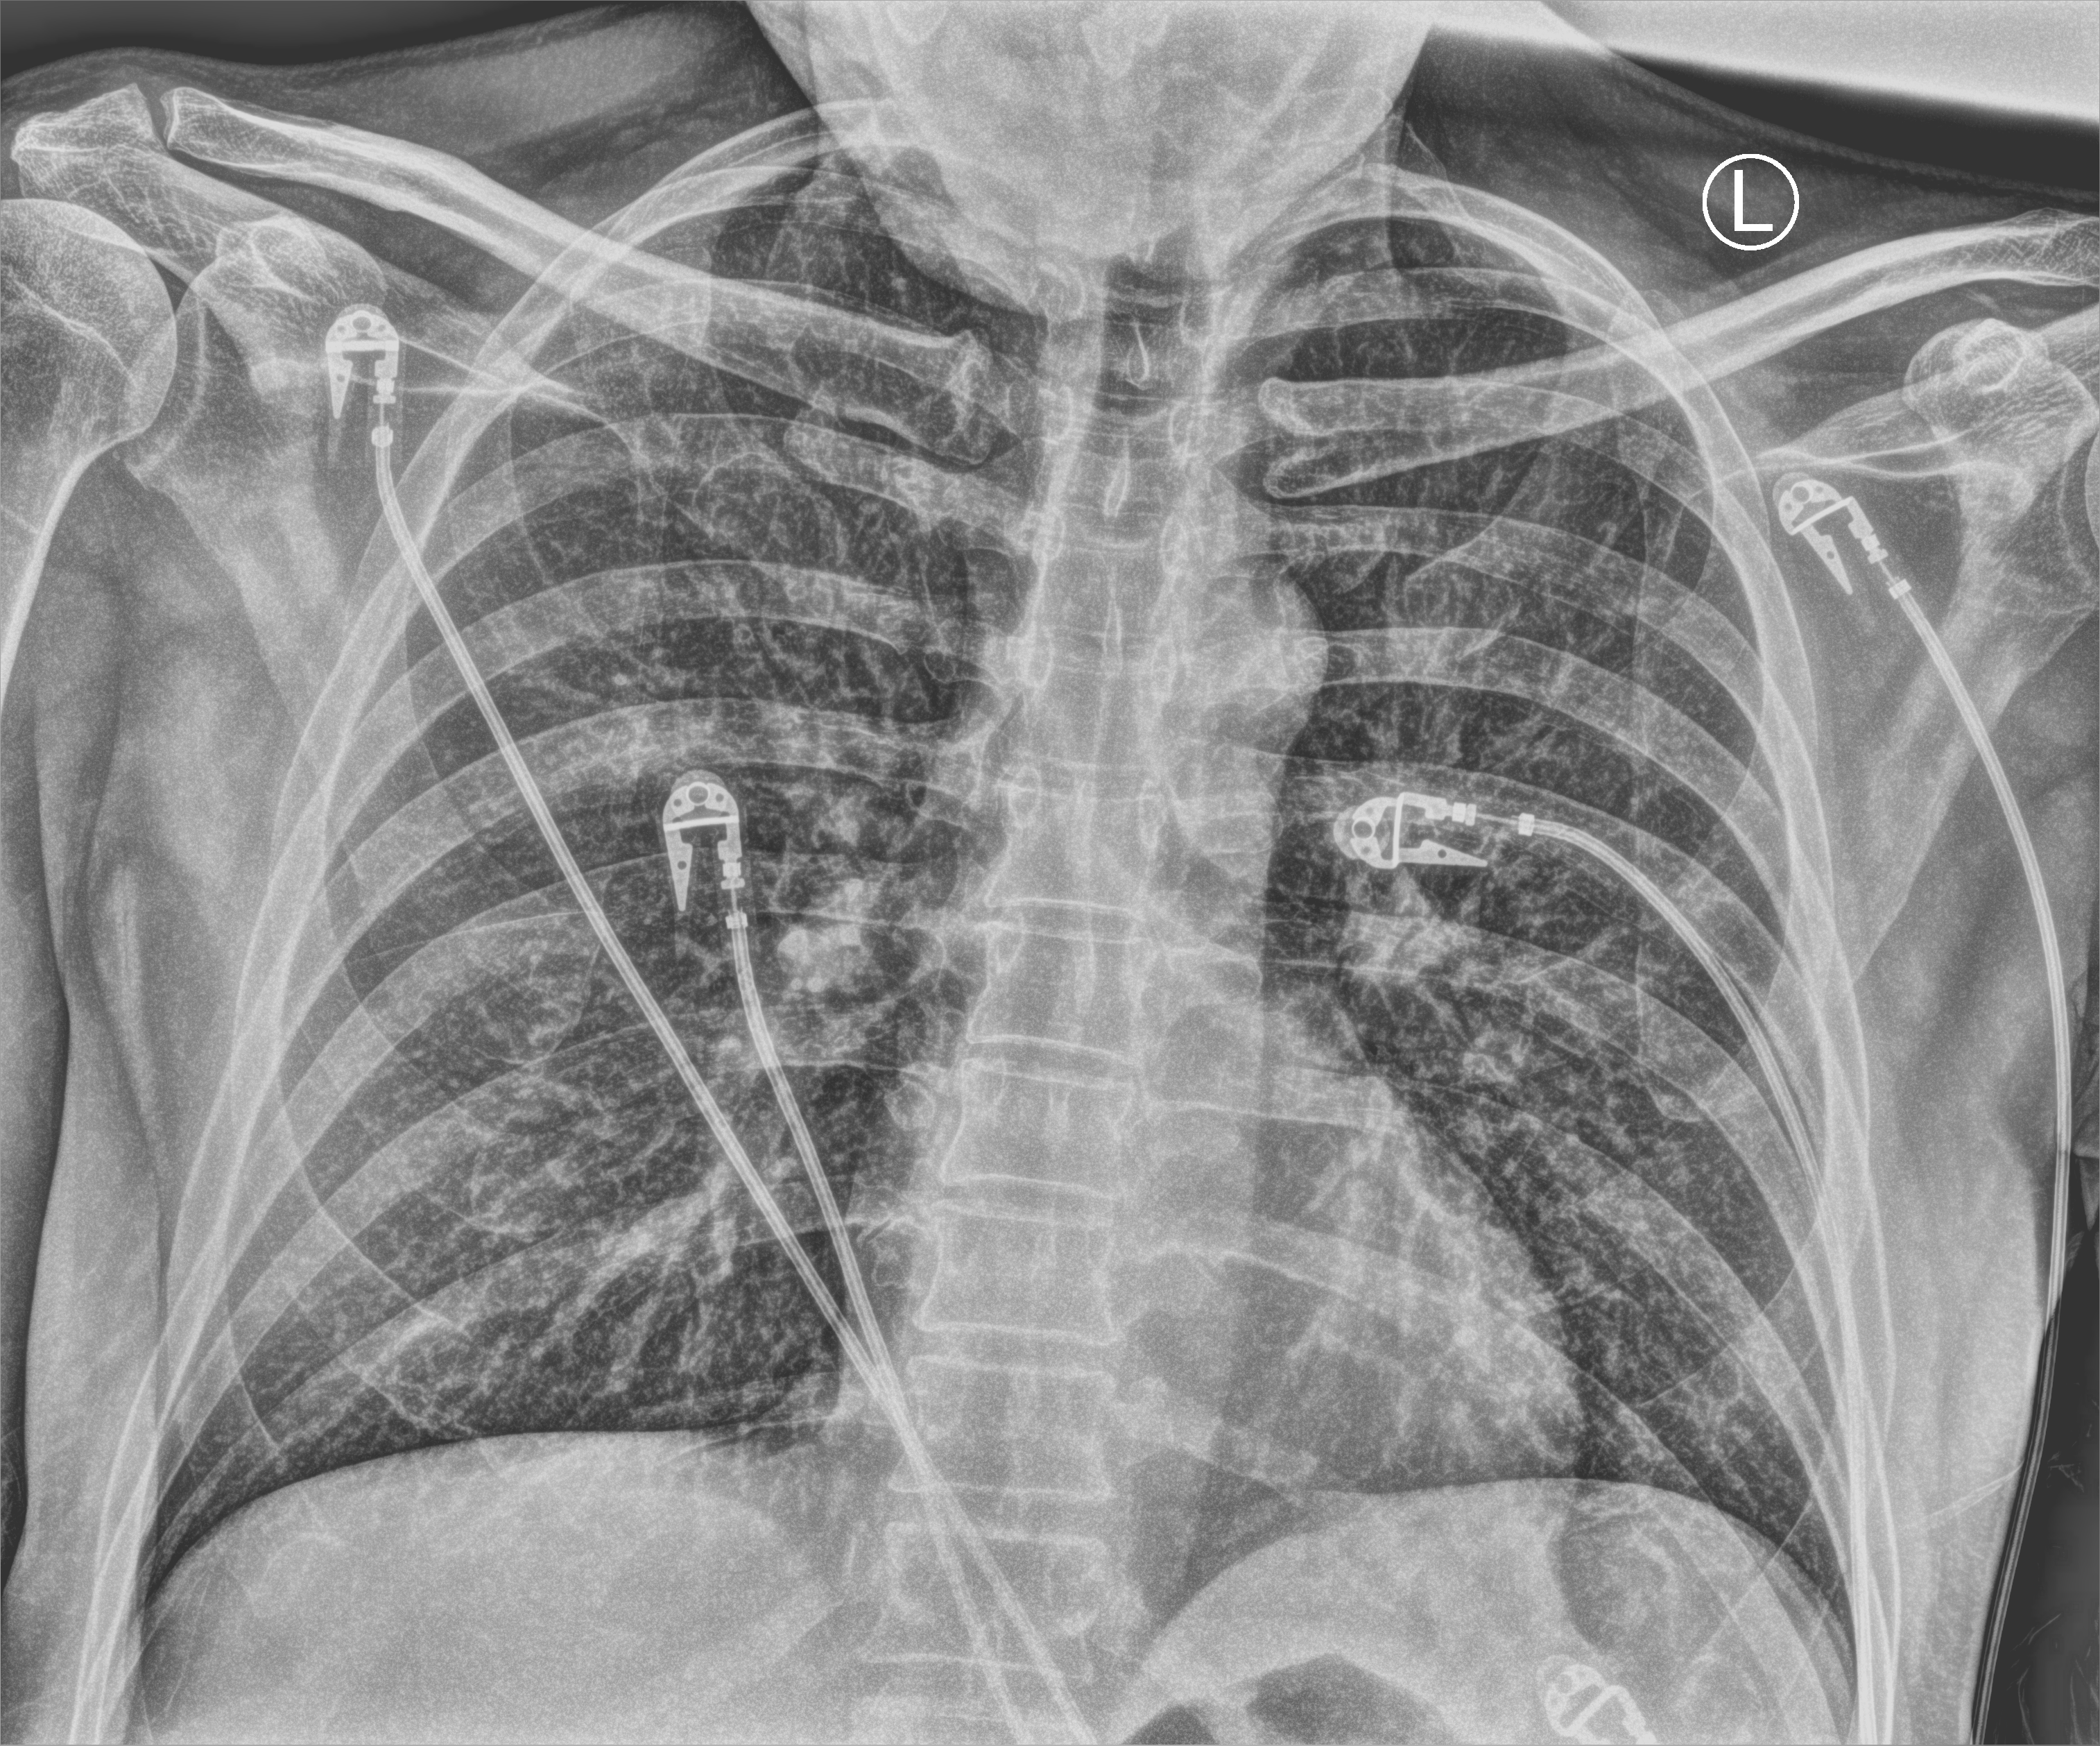
Bedside chest radiograph (computed radiography); anteroposterior (AP) projection. Patient hospitalised with COVID-19; male, aged 18–59 years.
Hospital-stay facts (about this admission, not read from this image; timing relative to this image not recorded): diabetes (admission record): yes.